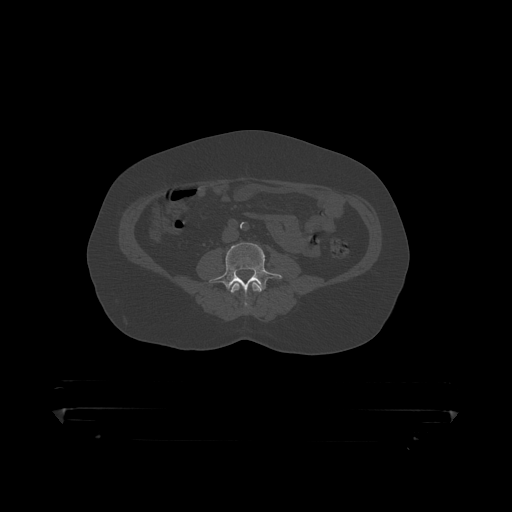
CT including the spine, one axial slice. Position 70 of 390 along the scan axis. 120 kVp. Bone window (W 1800 / L 400 HU). 1.25 mm slice thickness. 512 × 512 image matrix, field of view 650 × 650 mm. Patient: male, 60 years. From the clinical record (not read from this slice): primary cancer: prostate.
Annotated regions visible in this slice (semi-automatic segmentation, software-assisted and operator-edited):
- L3 vertebra: bounding box (x1, y1, x2, y2) in pixels: (230, 280, 264, 309)
- L4 vertebra: (209, 243, 282, 292)